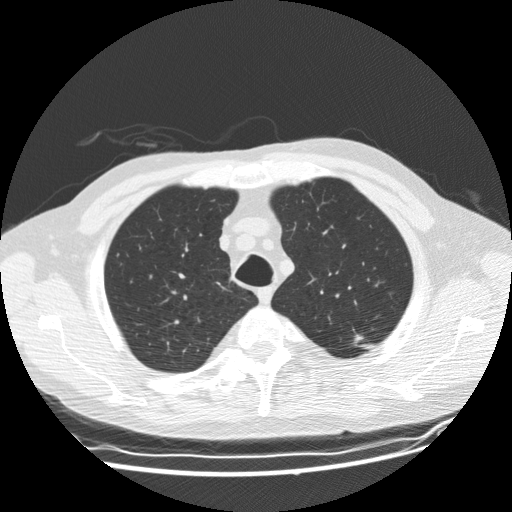
Low-dose screening chest CT, one axial slice. Slice 148 of 177 in the series (ordered by position). Reconstruction kernel STANDARD. 120 kVp. Lung window (W 1500 / L -600 HU). 2.5 mm slice thickness. 512 × 512 image matrix, field of view 360 × 360 mm.
Structures marked on this image (manually delineated by an expert):
- lesion 1 (tumor, upper lobe of left lung): bounding box (x1, y1, x2, y2) in pixels: (354, 334, 364, 342)